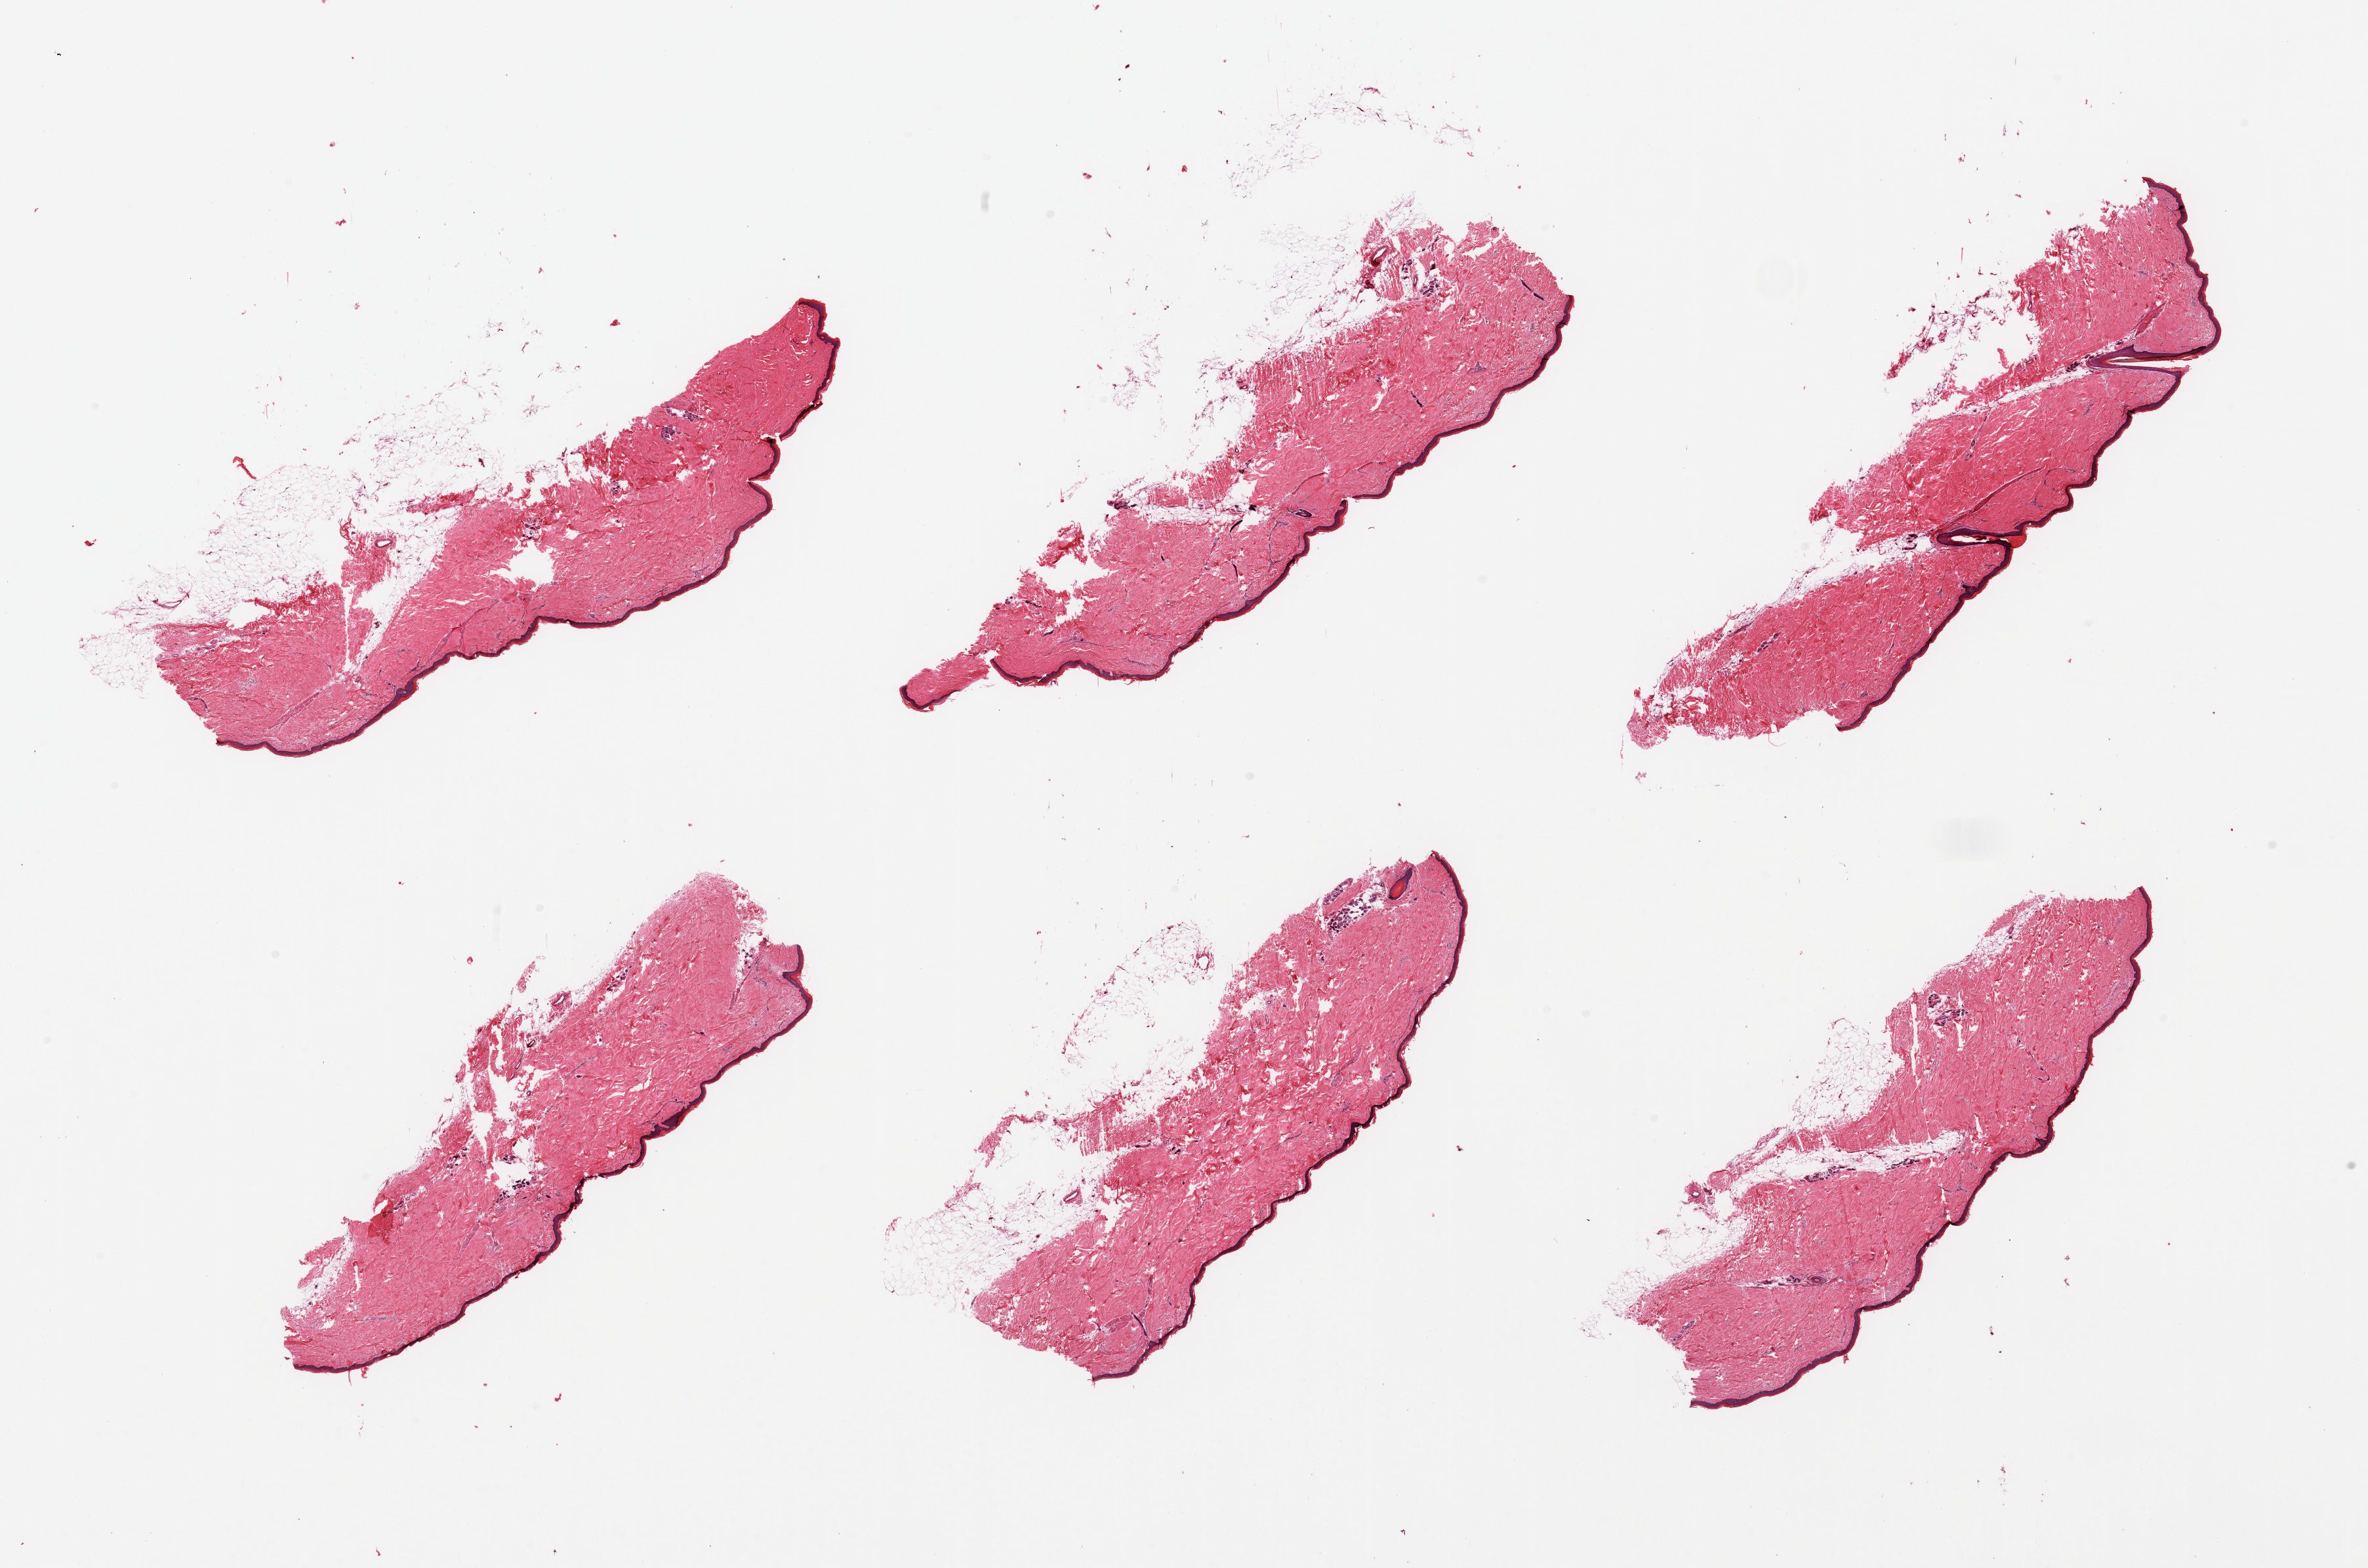
Whole-slide image, hematoxylin and eosin (H&E) stain, low-resolution overview of the scanned area, about 28.5 x 18.9 mm (from a 20x scan), PAXgene-fixed, paraffin-embedded tissue, sampled site (target tissue): skin of lower leg, tissue donor sample. Donor: female.
Pathologist's review note for this sample: 6 pieces; well trimmed; 5% dermal fat.